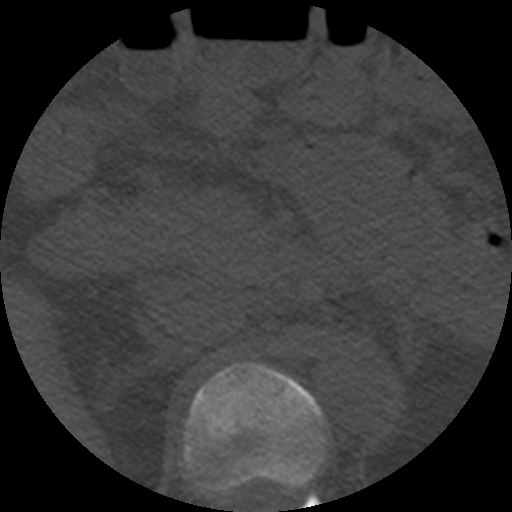
CT including the spine, one axial slice; slice 226 of 508 in the series (ordered by position); 120 kVp; bone window (W 1800 / L 400 HU); 1.25 mm slice thickness; 512 × 512 image matrix. Patient age 57 years. Case-level facts recorded for this patient, not image findings: primary cancer: prostate.
Outlined on this slice (semi-automatically segmented with operator editing):
- T12 vertebra: bounding box [x1, y1, x2, y2] px = [184, 362, 327, 506]